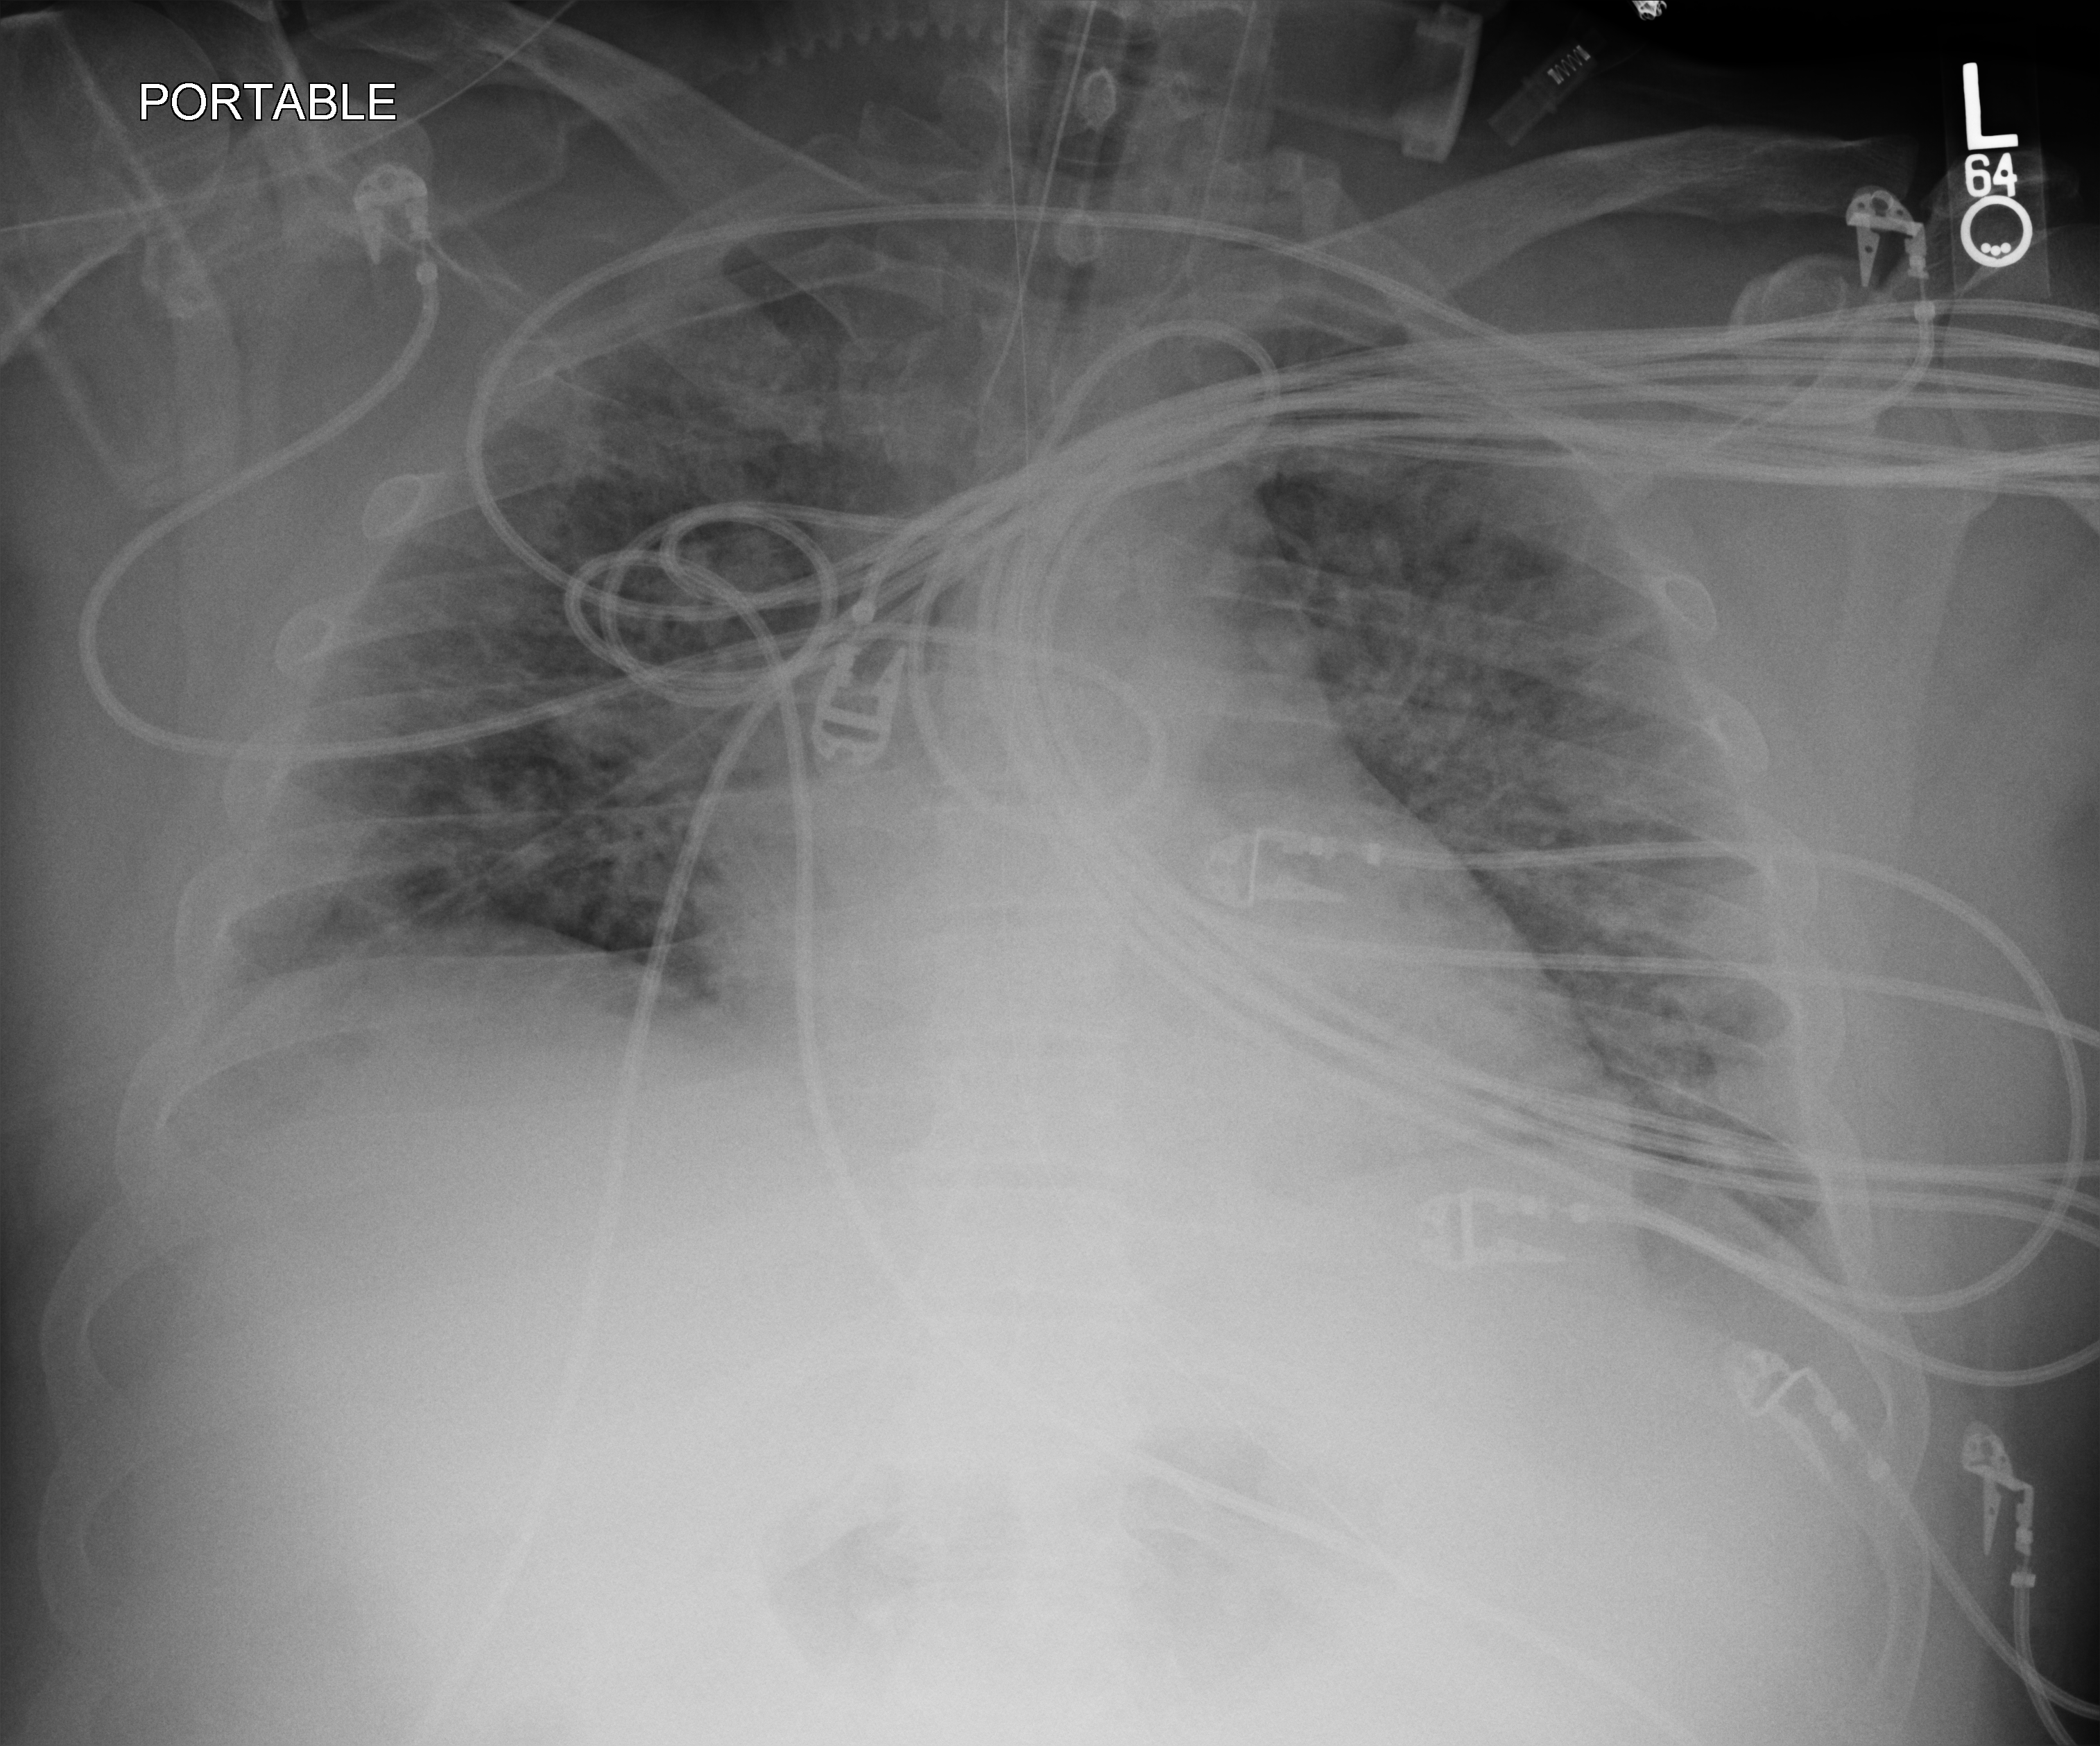
Portable chest radiograph. Patient hospitalised with COVID-19, aged 18–59 years.
Admission-level facts for this patient (not findings on this image; timing relative to this image not recorded):
- admitted to intensive care during this hospital stay: yes